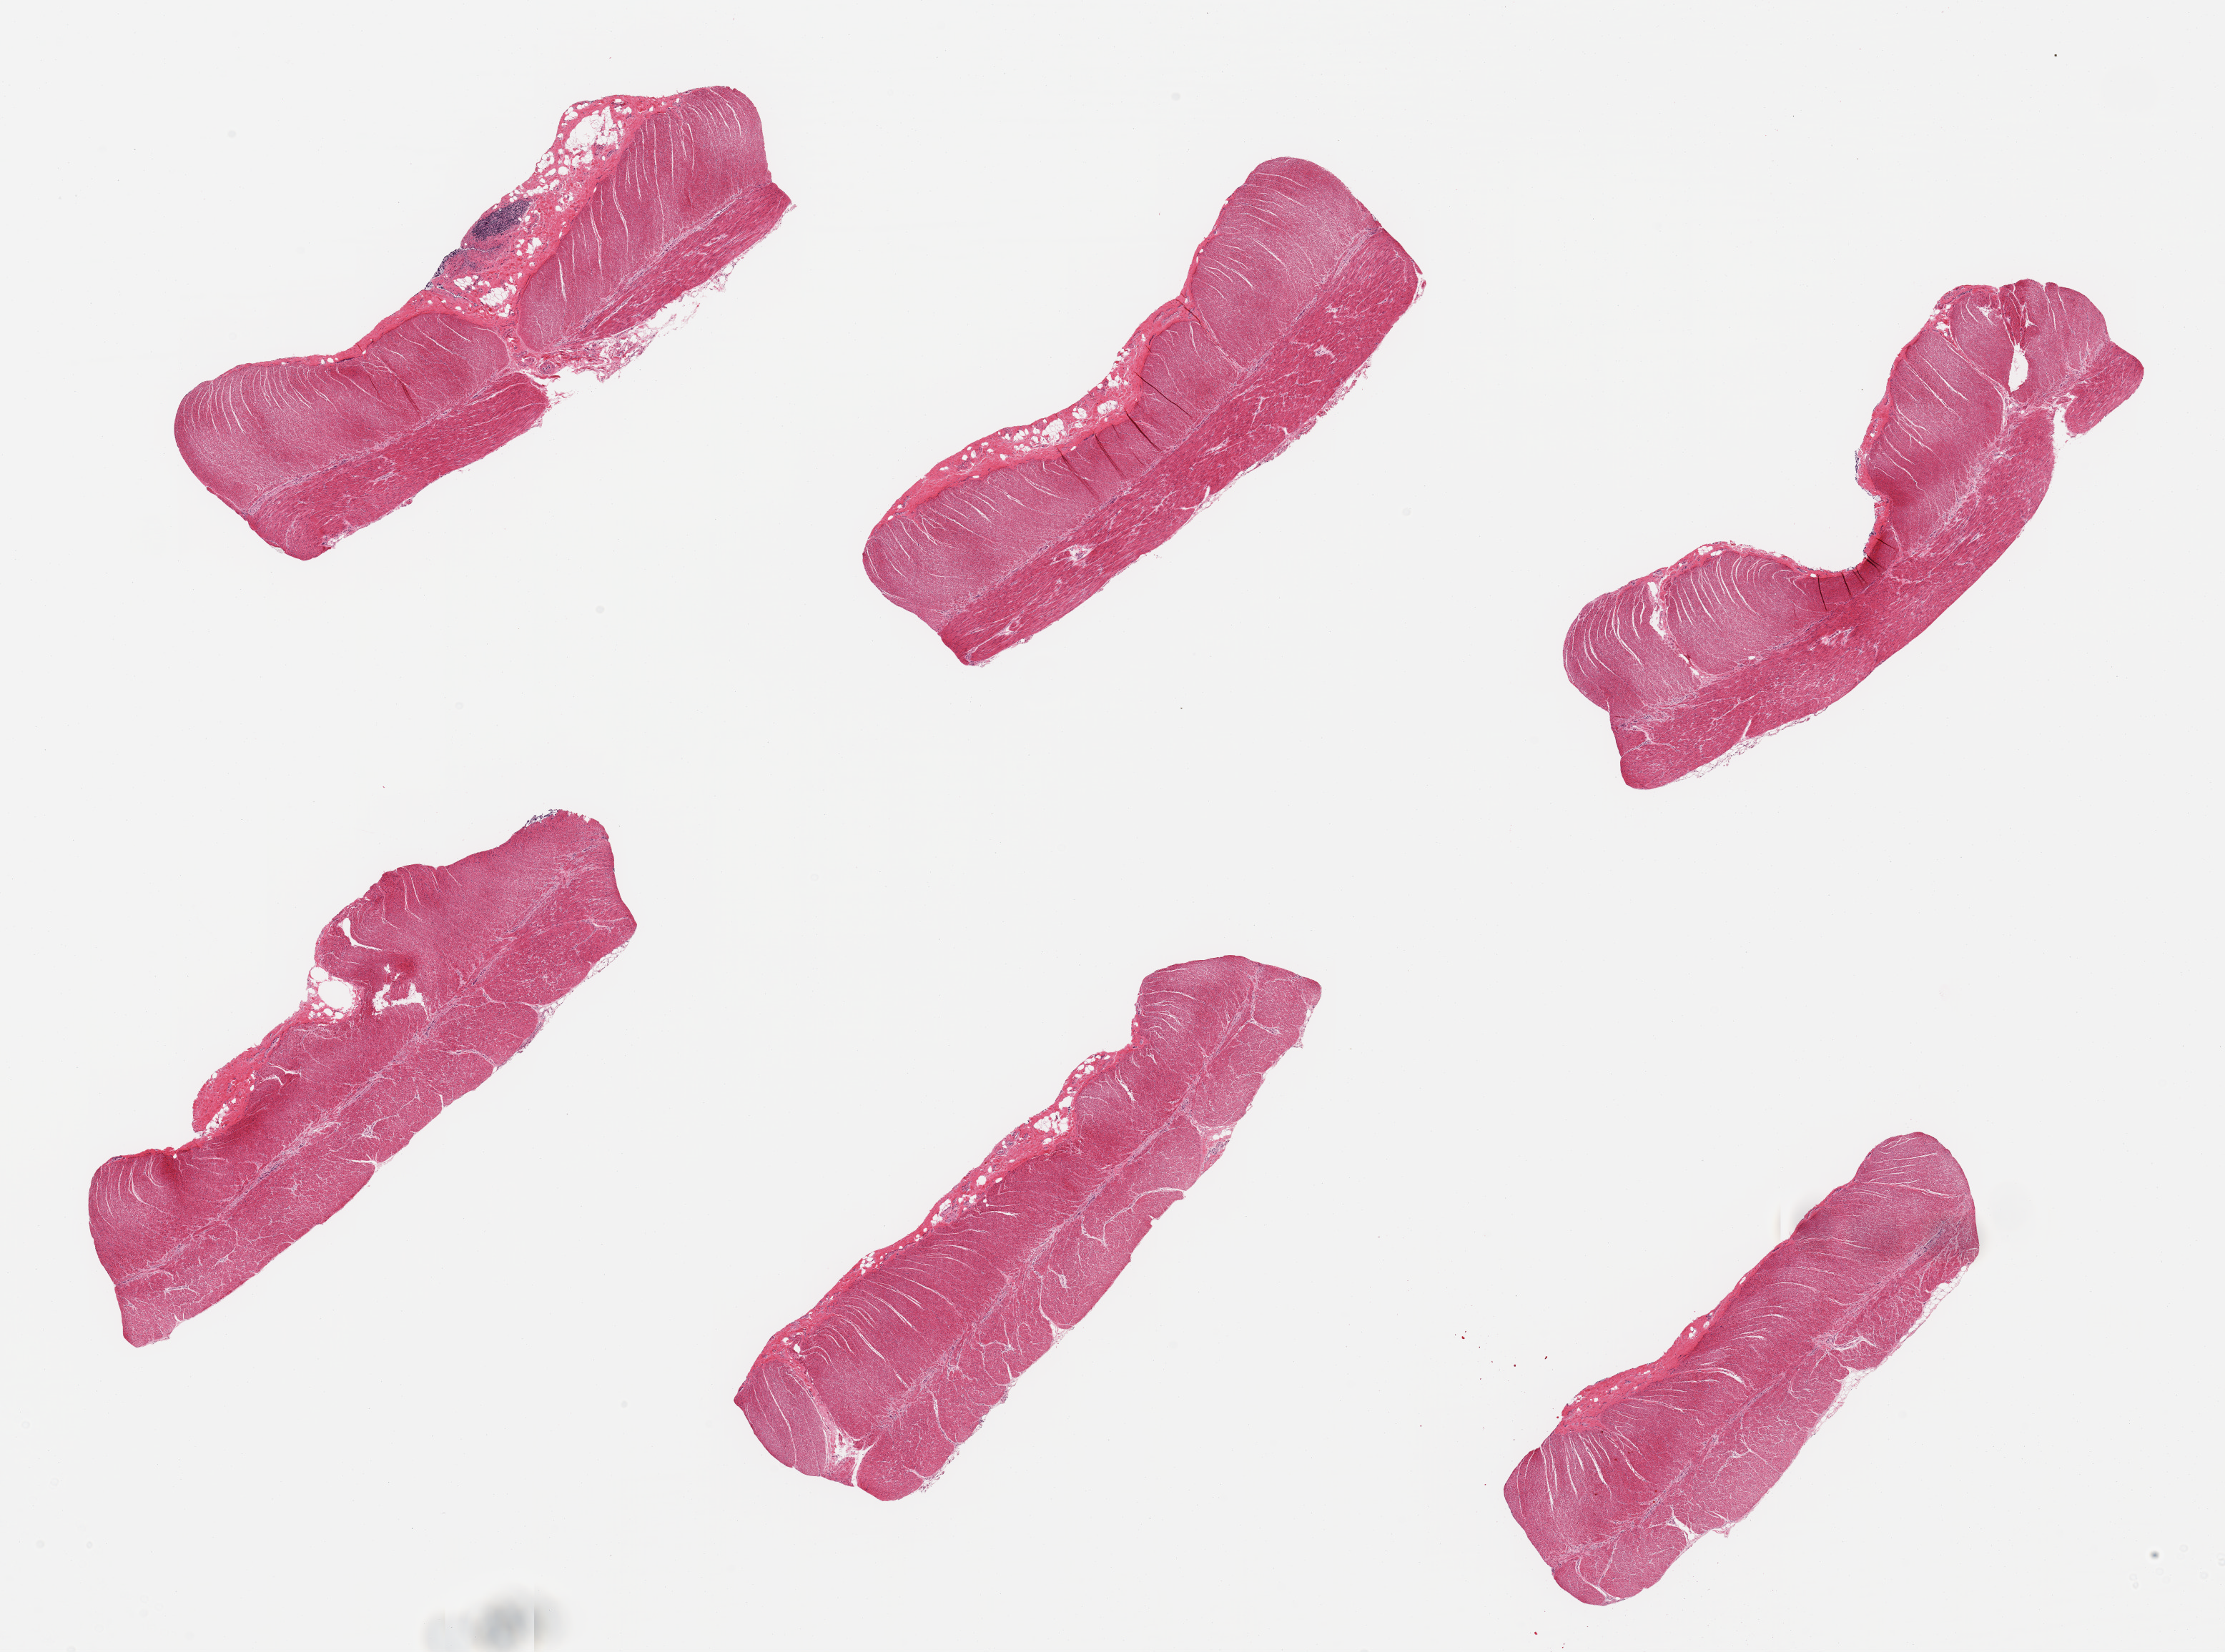
Digitized H&E-stained section, brightfield — a low-resolution overview of the entire scanned area, about 24.6 x 18.3 mm. PAXgene-fixed, paraffin-embedded tissue. Sampled site (target tissue): sigmoid colon. Donor tissue sample. Donor sex: male.
• review note (as recorded): 6 pieces, confirmed target muscularis